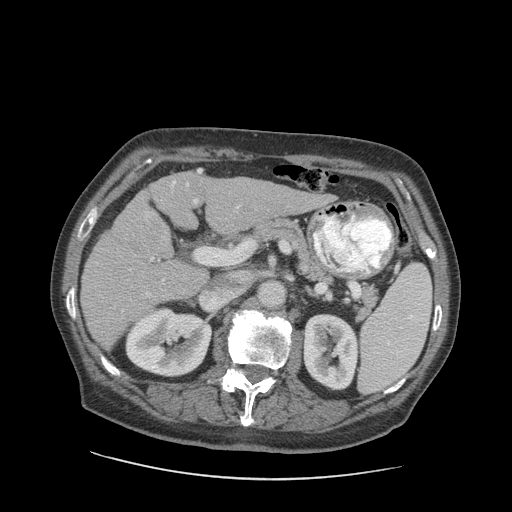
Contrast-enhanced abdominal CT (liver protocol), one axial slice. Reconstruction kernel STANDARD. 140 kVp. Soft-tissue window (W 400 / L 40 HU). 2.5 mm slice thickness. 512 × 512 image matrix, field of view 420 × 420 mm. From the clinical record (not read from this slice): diagnosis: hepatocellular carcinoma (patient treated with transarterial chemoembolisation; whether this scan precedes or follows treatment is not stated here); TNM stage (as recorded): Stage-I; Child-Pugh class: A; tumour nodularity: uninodular; tumour size: 4.6 cm.
Outlined on this slice (semi-automatically segmented with operator editing):
- liver parenchyma outside the tumour (the mass and vessels are separate outlines, so this box may not span the whole liver): bounding box (x1, y1, x2, y2) in pixels: (80, 170, 330, 350)
- mass: (129, 209, 172, 254)
- liver vessels: (96, 170, 240, 312)